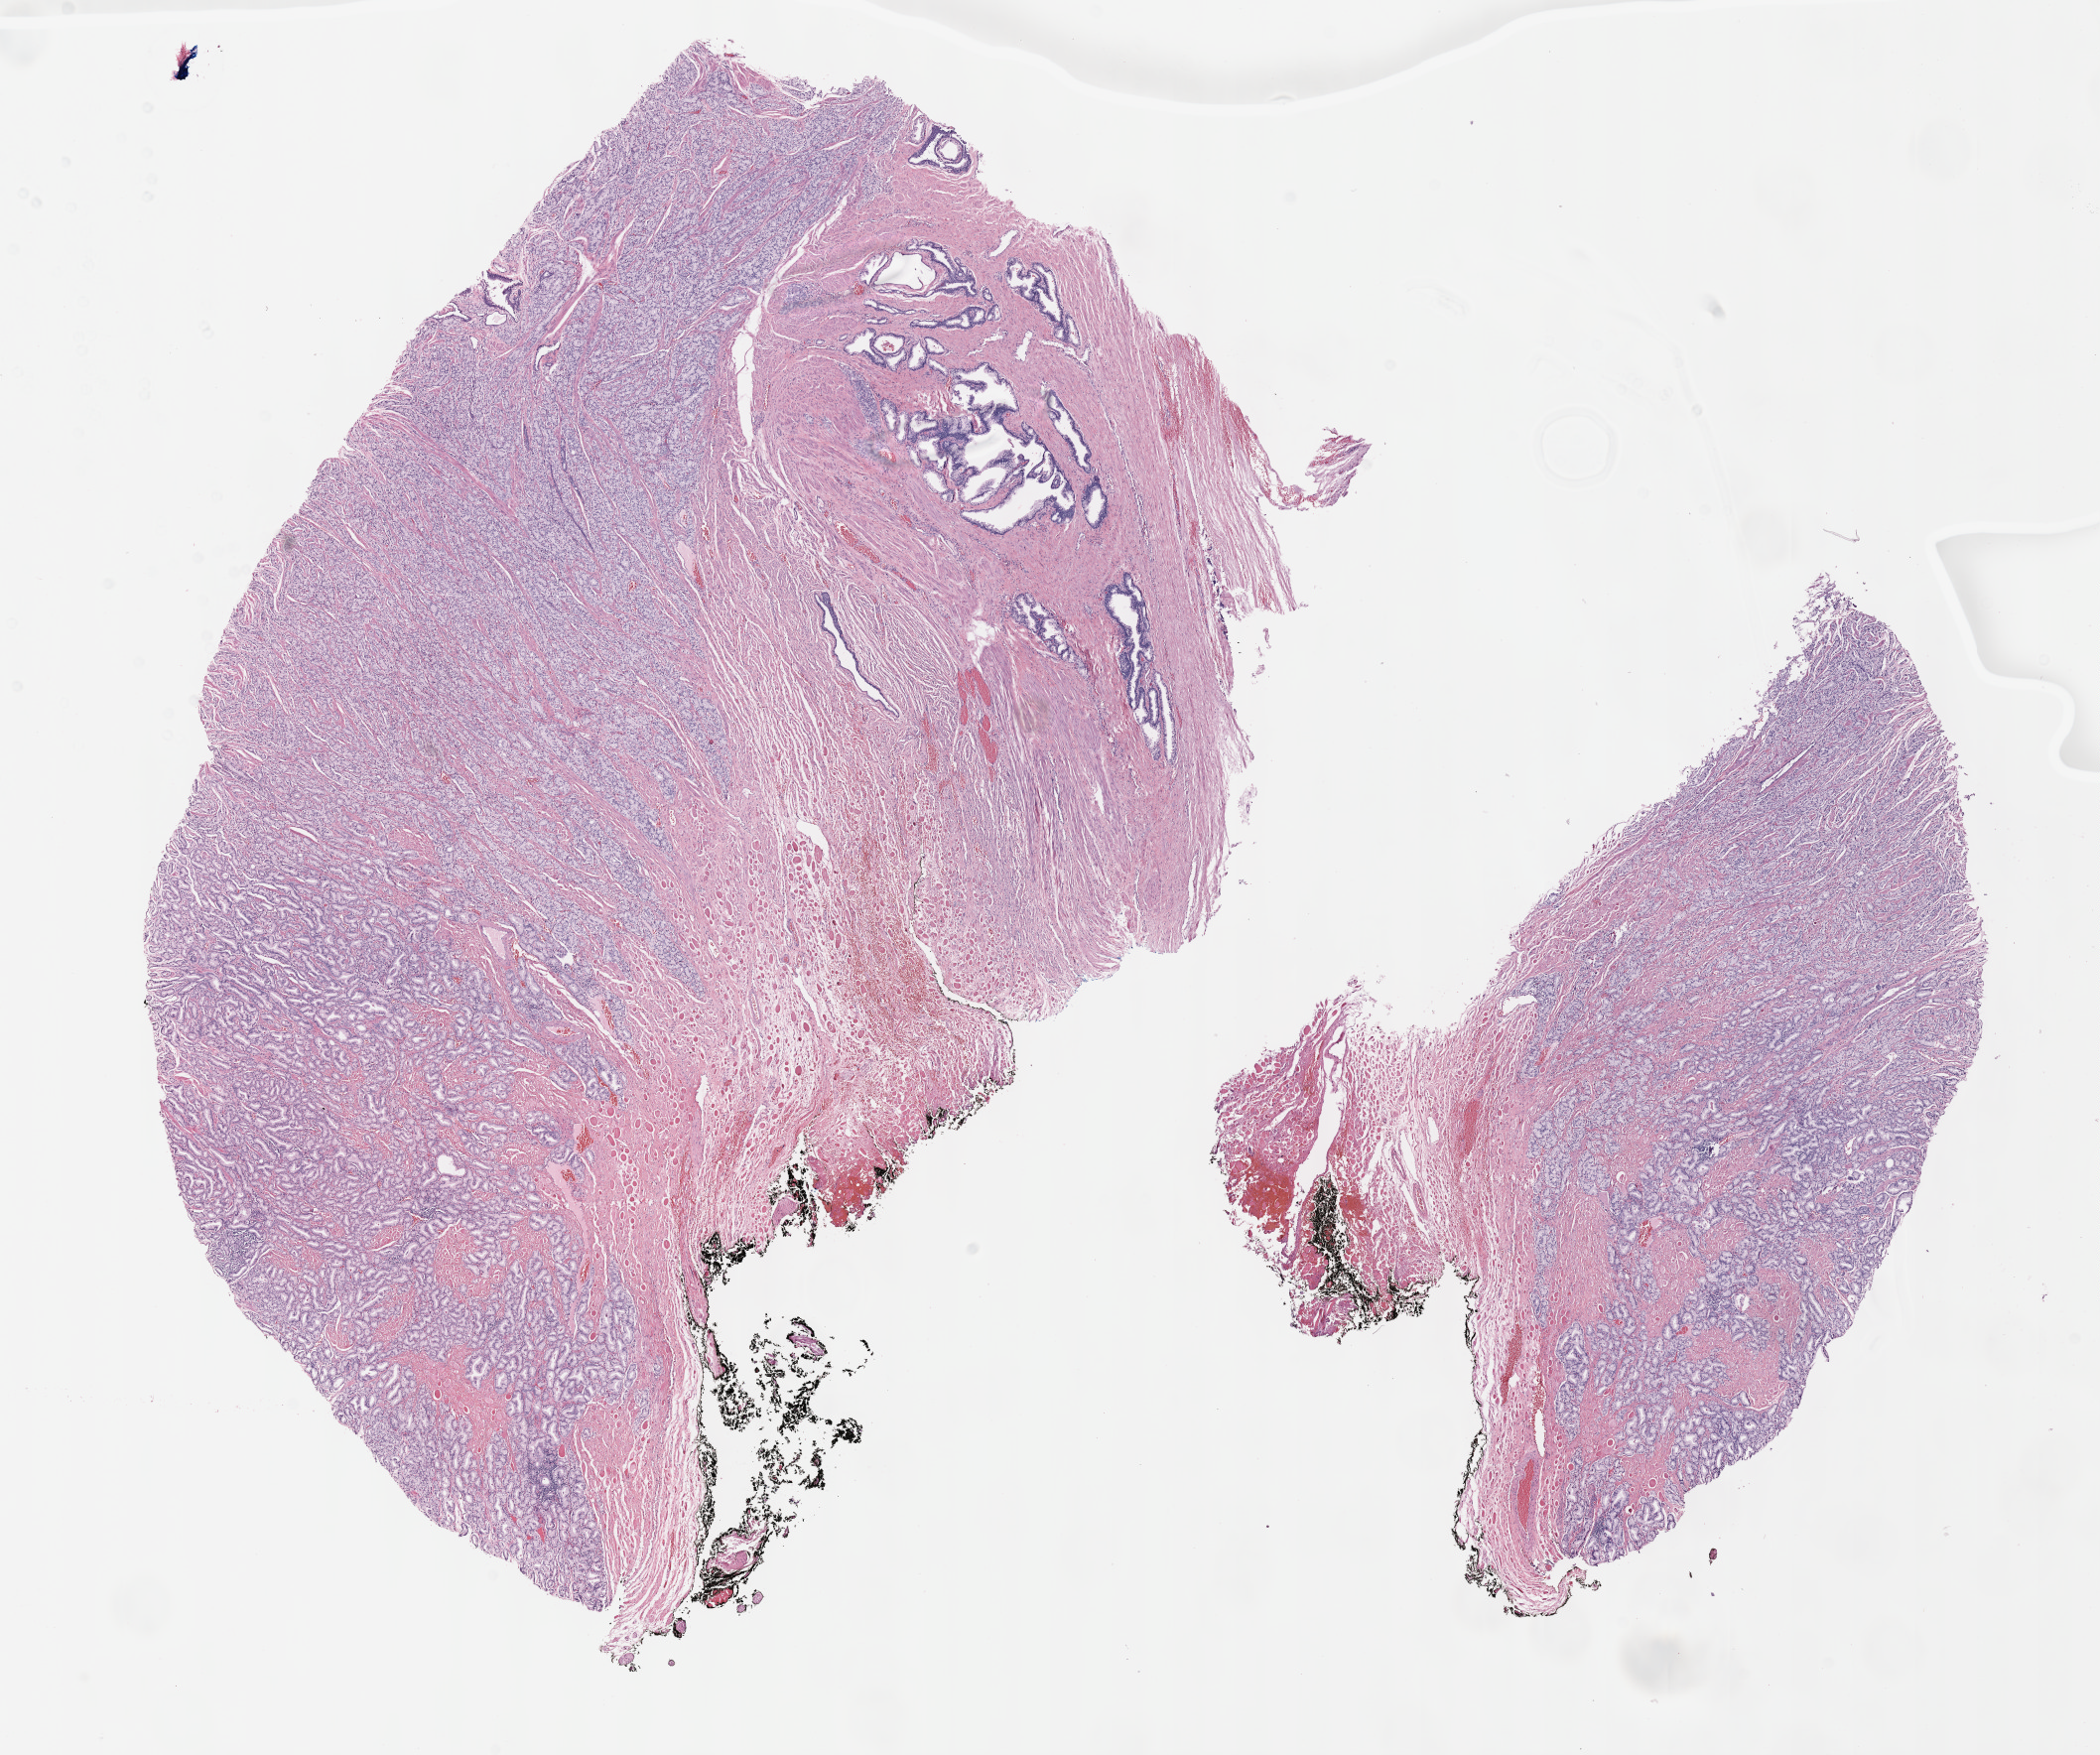
Whole-slide histology image, H&E-stained, shown as a low-resolution overview of the whole scanned area (about 17.1 x 14.3 mm, from a 40x scan). Formalin-fixed paraffin-embedded (FFPE) diagnostic section. Prostate, primary tumour sample. Male patient; age at initial diagnosis 70 years. Gleason score: 8 (4+4).
Laterality: bilateral. Histologic diagnosis: Adenocarcinoma, NOS. Lymph nodes positive (case pathology): 0 of 4 examined.